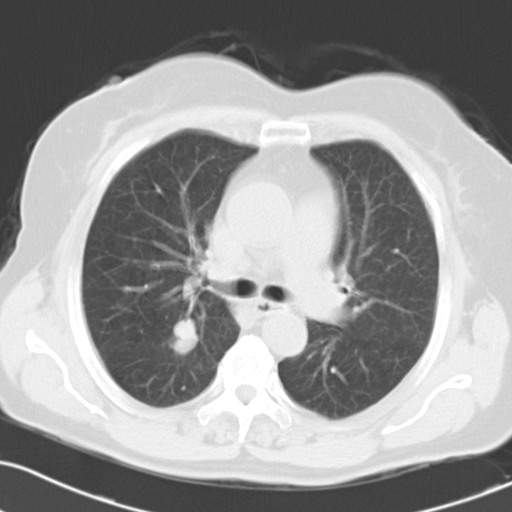
Chest CT, one axial slice. Position 18 of 27 along the scan axis. 120 kVp. Lung window (W 1500 / L -600 HU). 512 × 512 image matrix, field of view 323 × 323 mm. Female patient, age 70 years. Case-level facts recorded for this patient, not image findings: clinical TNM (as recorded): T1c N3 M0; histopathological grade: G3.
Annotated regions visible in this slice (rectangle marked by the reading radiologist):
- lung tumour (recorded histology: small cell carcinoma): bounding box <162,315,208,360> (left, top, right, bottom; pixels)